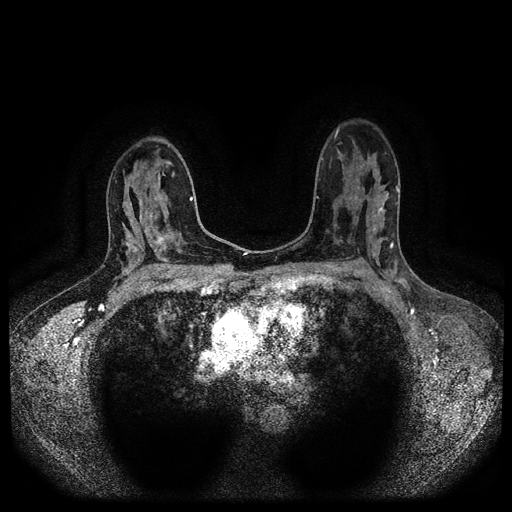
Breast MRI (dynamic contrast-enhanced, multi-phase), one axial slice; position 65 of 116 along the scan axis; dynamic contrast-enhanced series, time point 2 of 5 at this slice position (early post-contrast); 1.5 T; TE 2.6 ms, TR 5.4 ms; 512 × 512 image matrix, field of view 340 × 340 mm. Female patient, age 47 years.
Structures marked on this image (semi-automatic segmentation, software-assisted and operator-edited):
- breast lesion (labelled 'tumour' in the annotation; benign lesions carry a separate 'benign' label): box from (x=155, y=231) to (x=166, y=251) px